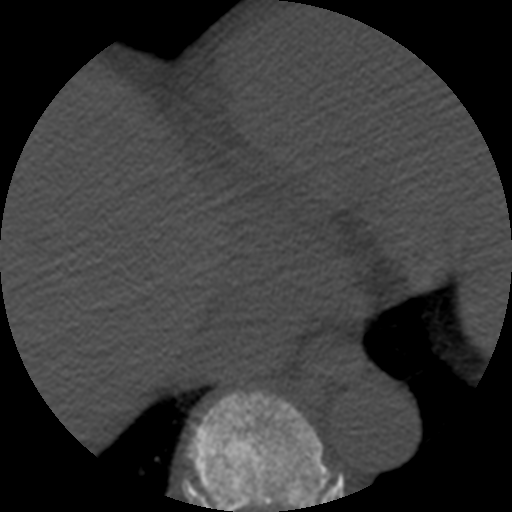
CT including the spine, one axial slice; slice 304 of 508 in the series (ordered by position); bone window (W 1800 / L 400 HU); 512 × 512 image matrix, field of view 160 × 160 mm. Patient age 57 years. Case-level facts recorded for this patient, not image findings: primary cancer: prostate.
Outlined on this slice (semi-automatic segmentation, software-assisted and operator-edited):
- T8 vertebra: bounding box [x1, y1, x2, y2] px = [186, 390, 330, 512]
- T9 vertebra: [335, 476, 342, 498]